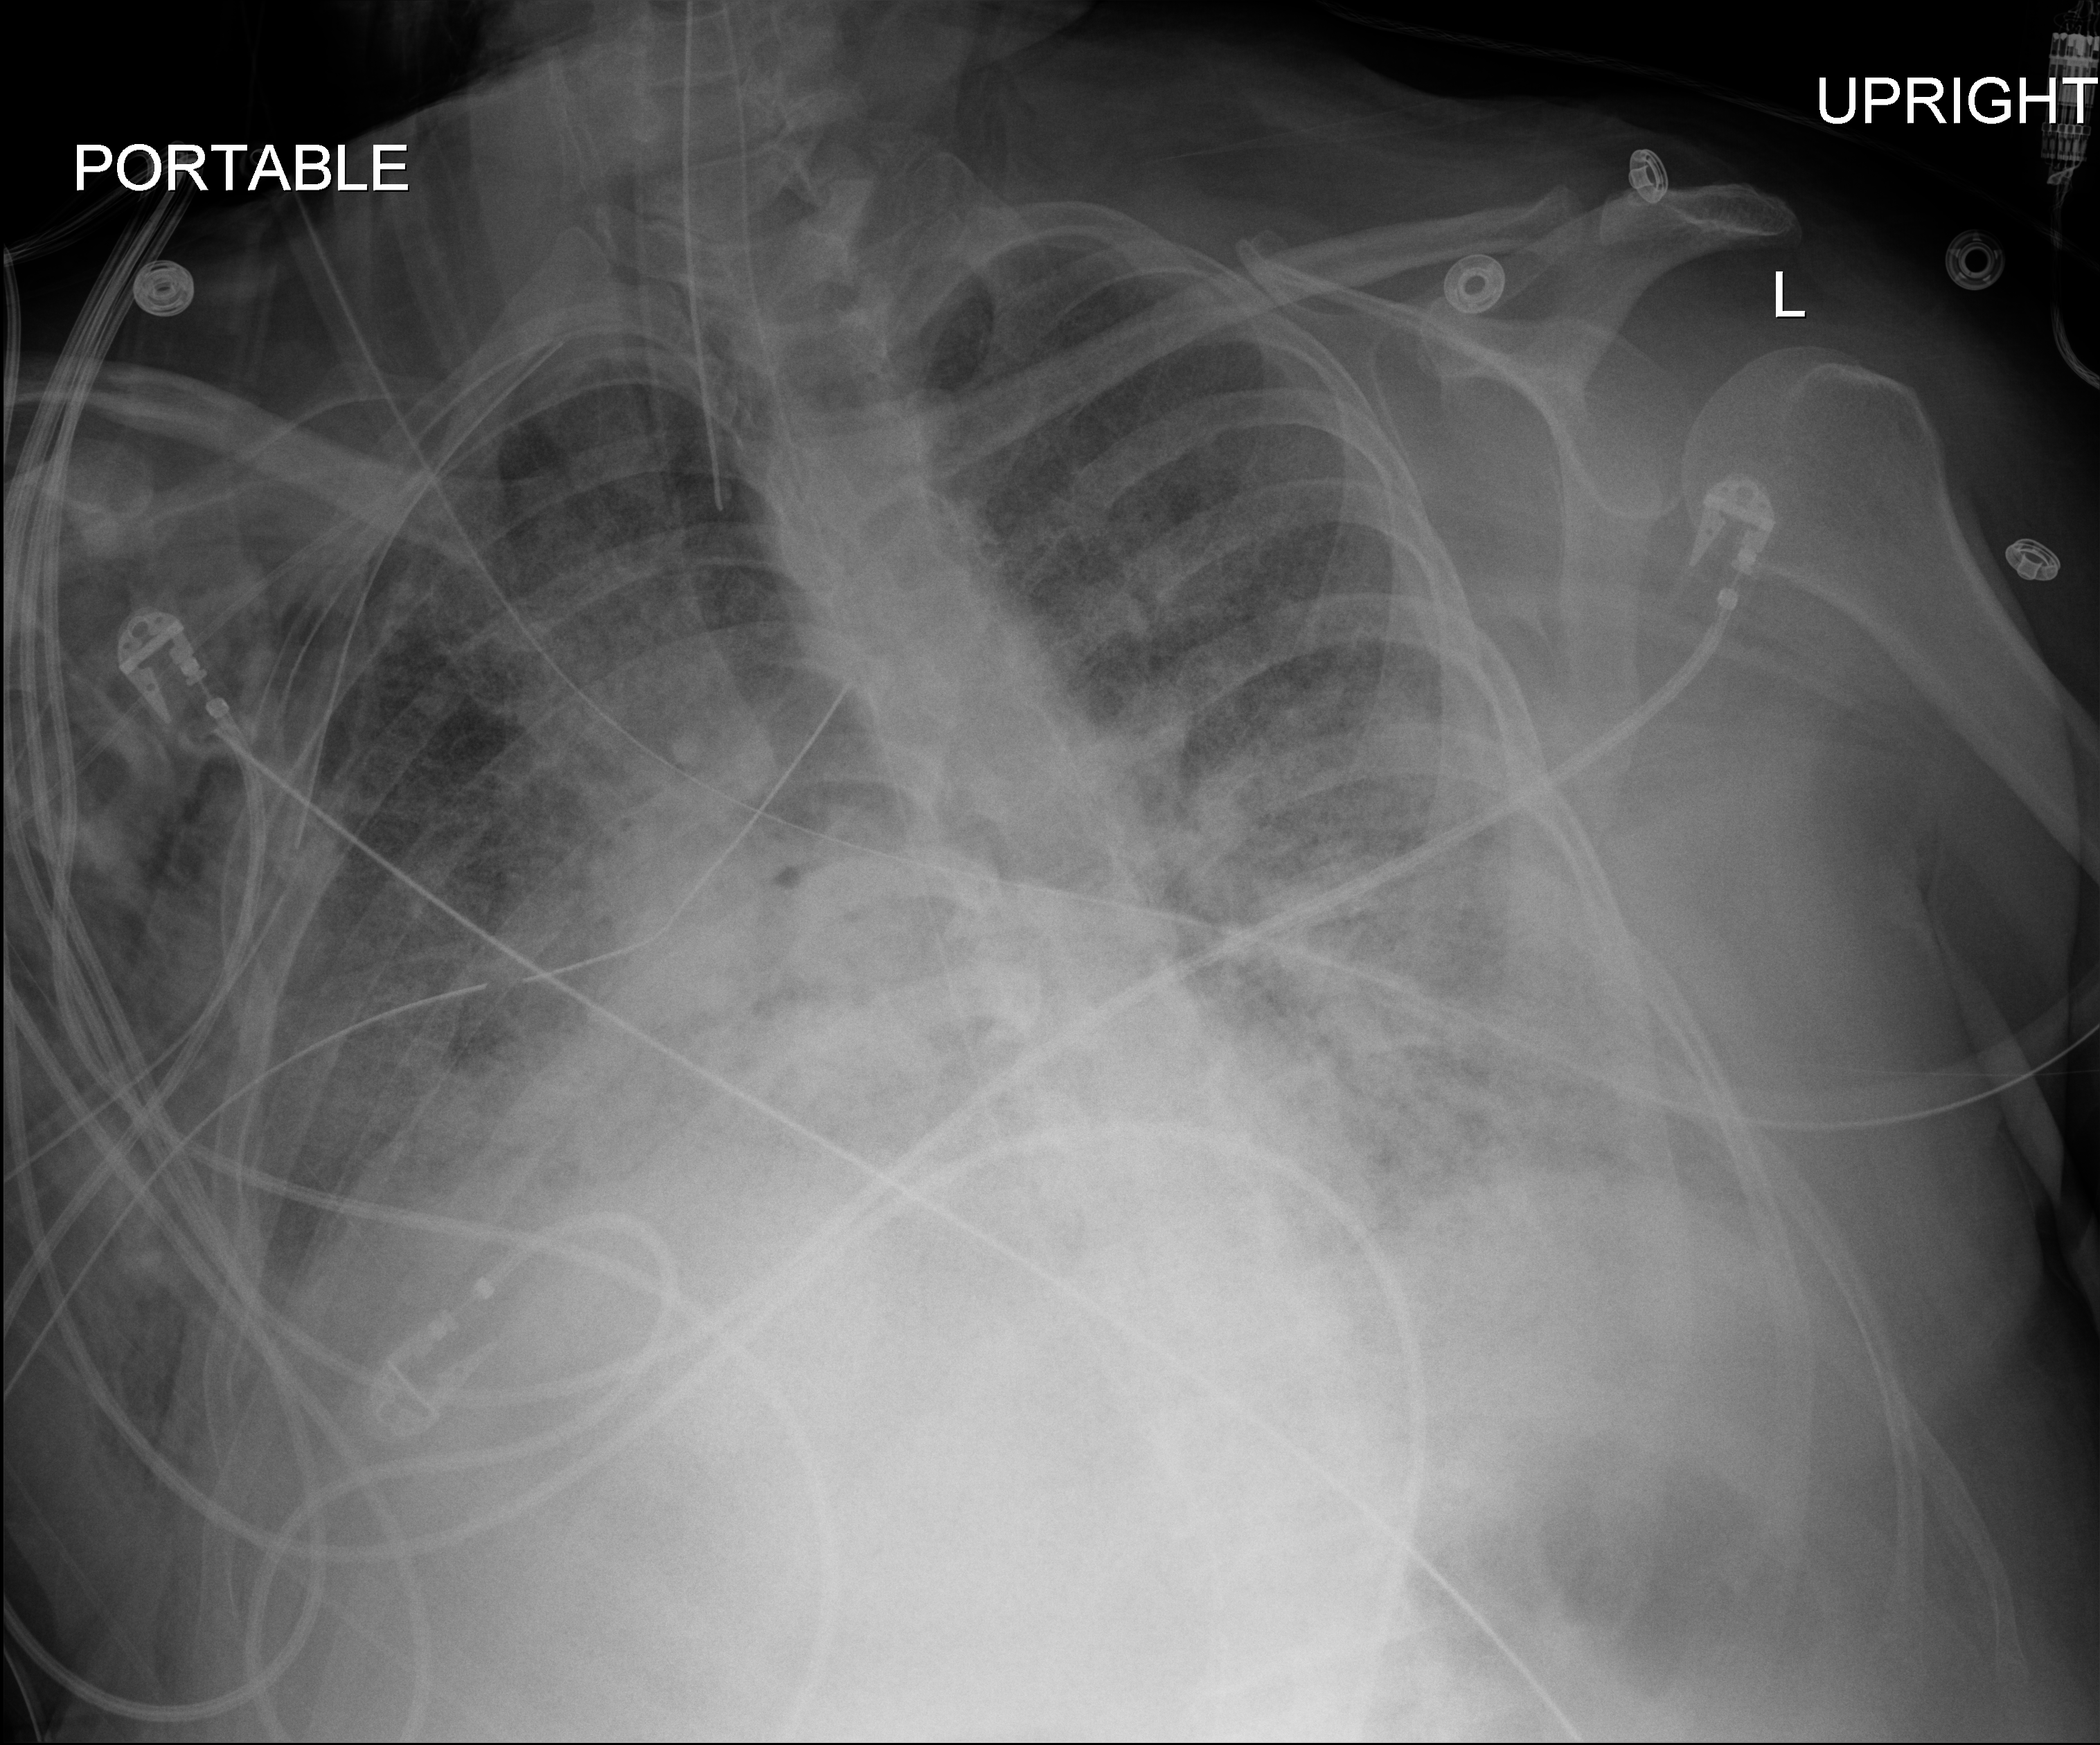
Portable chest radiograph, anteroposterior (AP) projection. Patient hospitalised with COVID-19, aged 18–59 years.
Hospital-stay facts (about this admission, not read from this image; timing relative to this image not recorded):
- admitted to intensive care during this hospital stay: yes
- other chronic lung disease (admission record): no